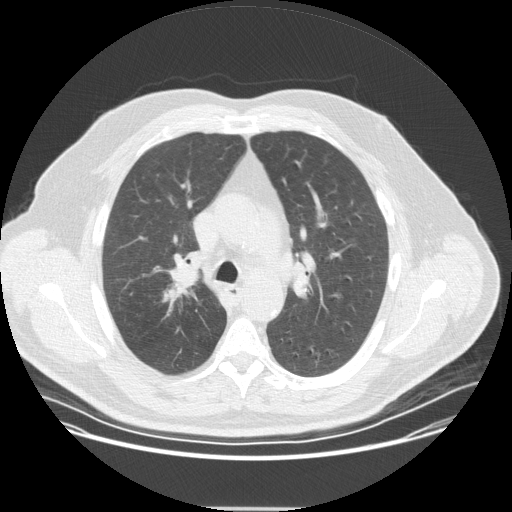
Low-dose screening chest CT, one axial slice. Reconstruction kernel STANDARD. 120 kVp. Lung window (W 1500 / L -600 HU). 2.5 mm slice thickness. 512 × 512 image matrix, field of view 419 × 419 mm.
Structures marked on this image (manually delineated by an expert):
- lesion 1 (tumor, upper lobe of right lung): bounding box [x1, y1, x2, y2] px = [162, 266, 201, 303]